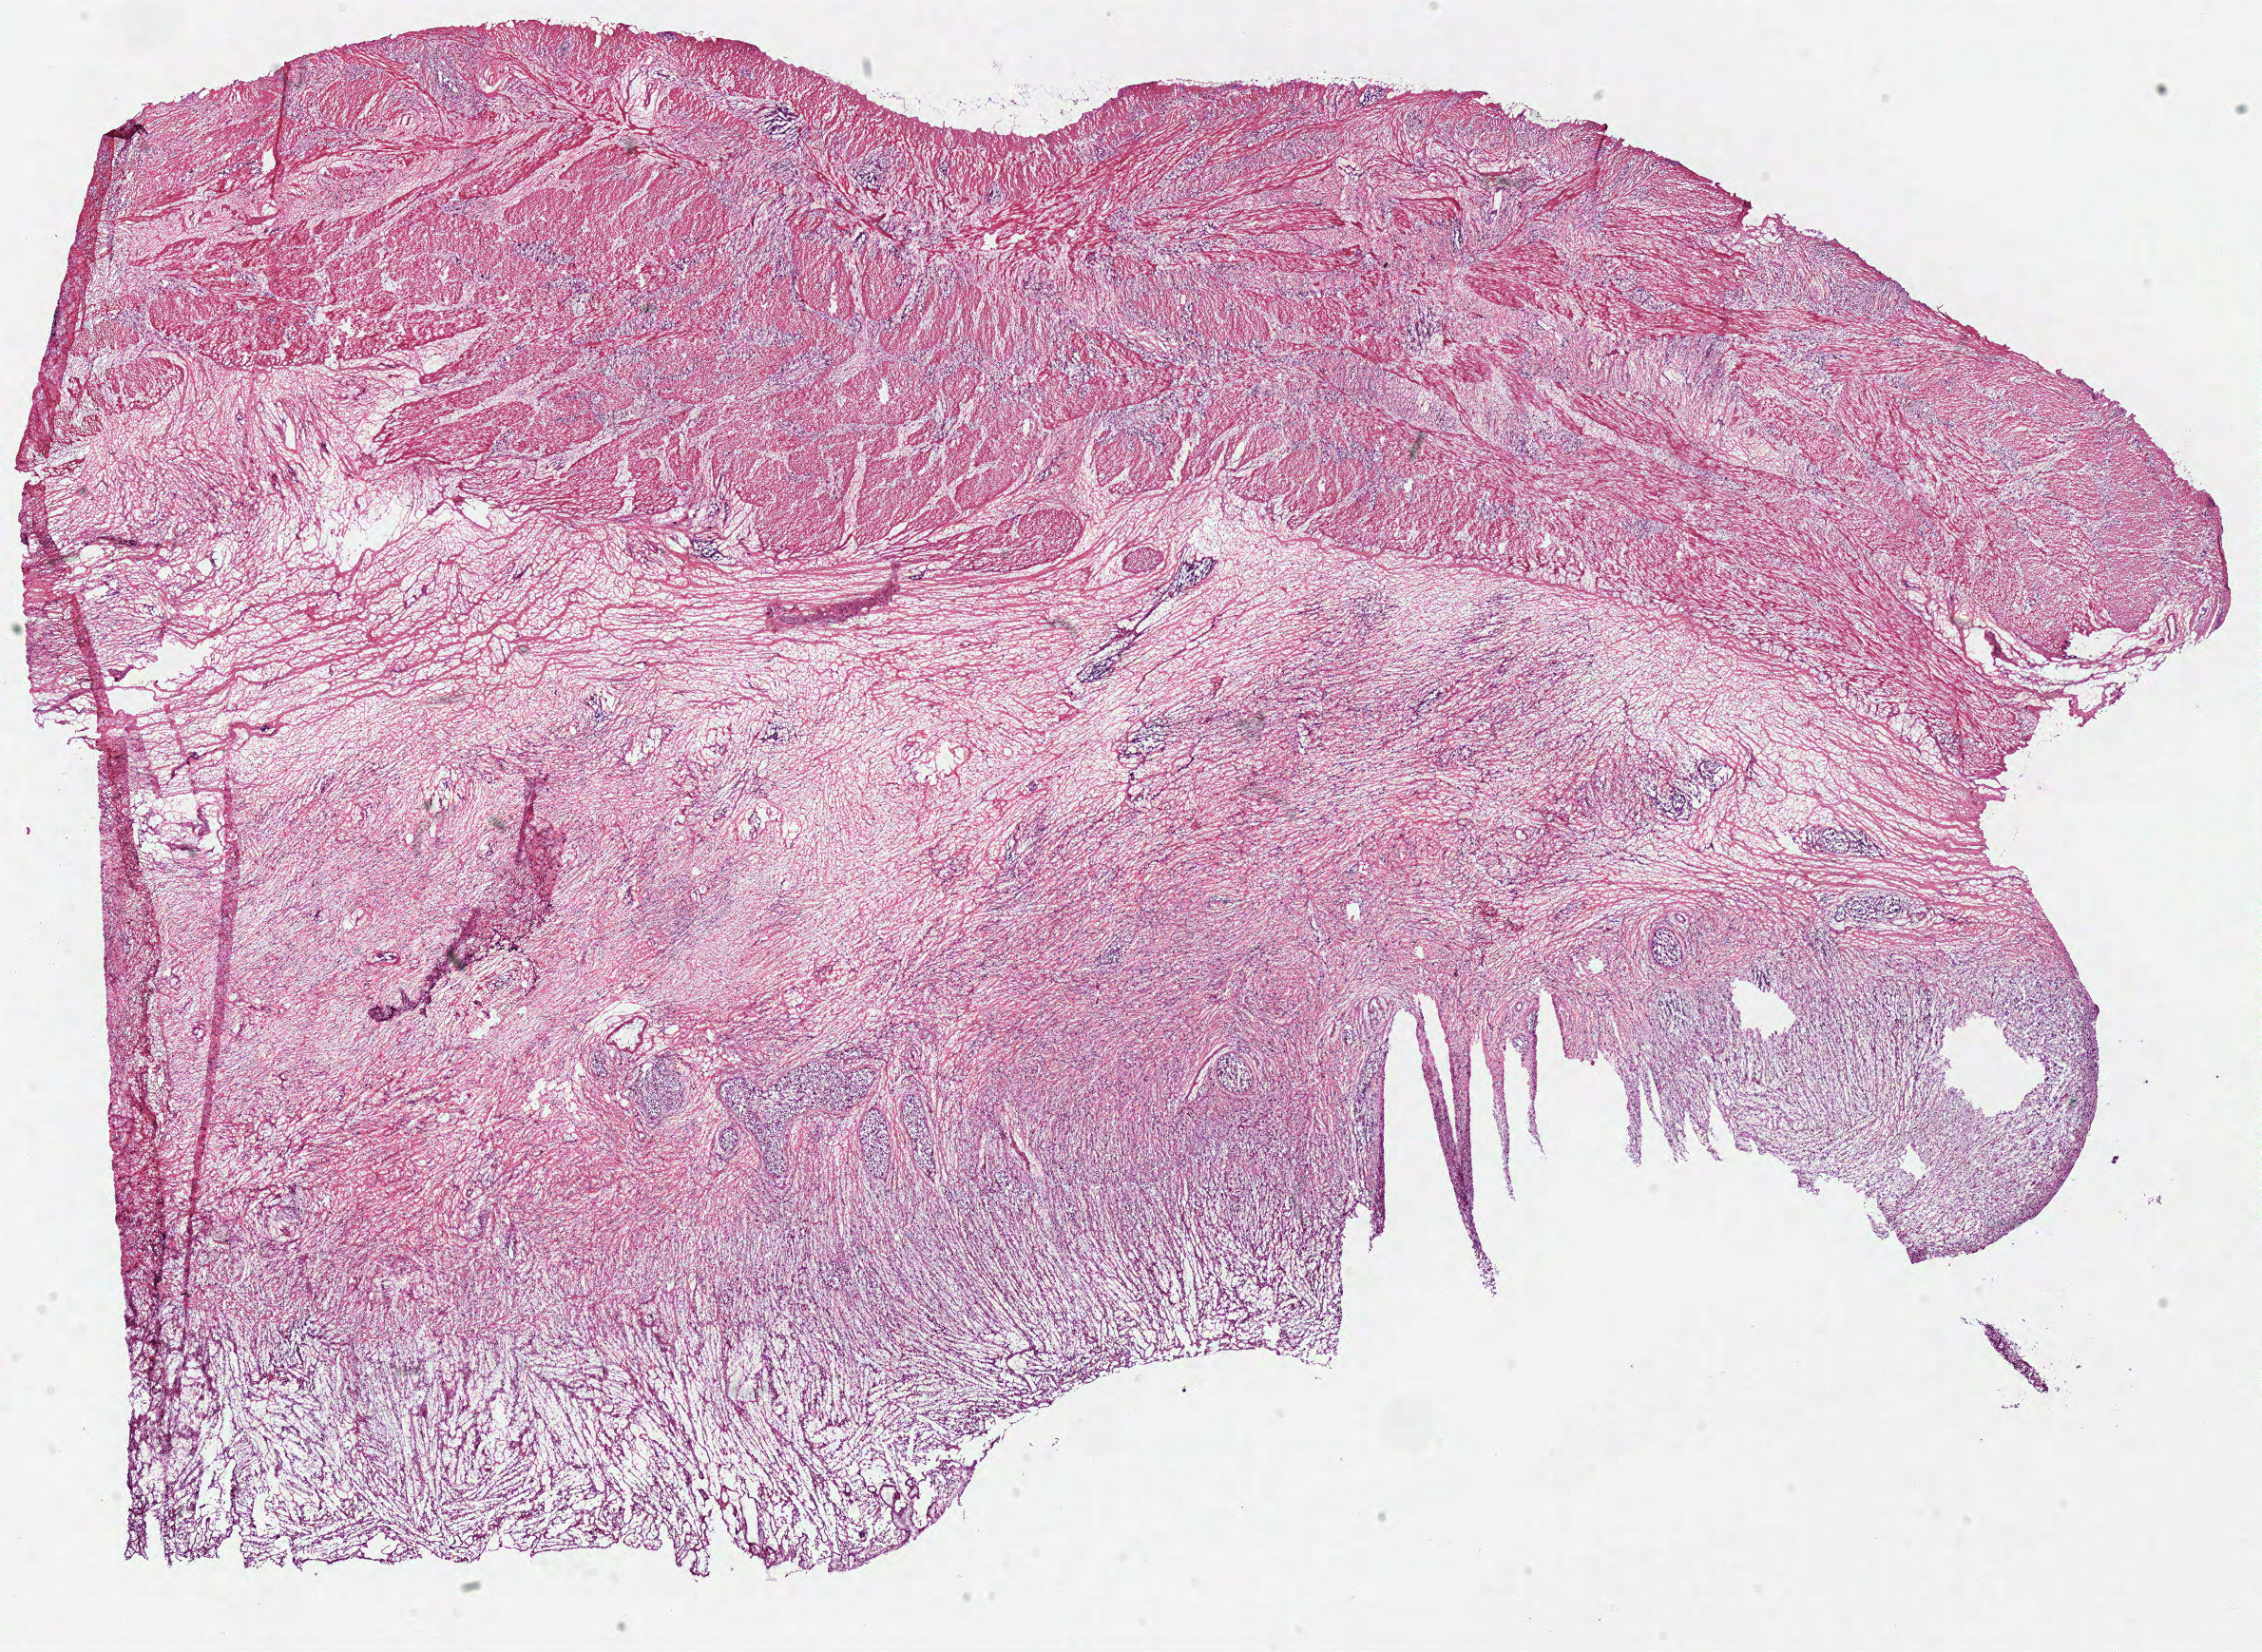
Whole-slide histology image, H&E, low-resolution overview of the scanned area, about 18.8 x 13.7 mm. Frozen section from the top of the tissue portion. Stomach, primary tumour sample. Patient: female, age at initial diagnosis 54 years.
Pathologic diagnosis: Carcinoma, diffuse type (body of stomach).